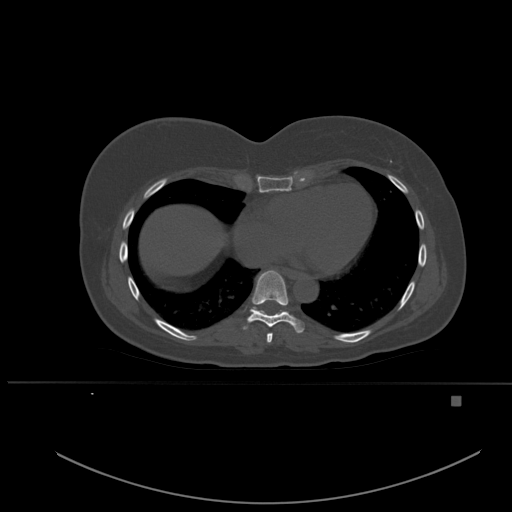
CT including the spine, one axial slice. Slice 320 of 651 in the series (ordered by position). Bone window (W 1800 / L 400 HU). 1.5 mm slice thickness. 512 × 512 image matrix. Patient: female, 49 years. Case-level facts recorded for this patient, not image findings: primary cancer: breast; vertebrae with lytic lesions (as recorded): L3, T12, L4.
Outlined on this slice (semi-automatically segmented with operator editing):
- T7 vertebra: bounding box [x1, y1, x2, y2] px = [266, 333, 273, 343]
- T8 vertebra: [242, 270, 304, 333]
- T9 vertebra: [250, 307, 258, 311]